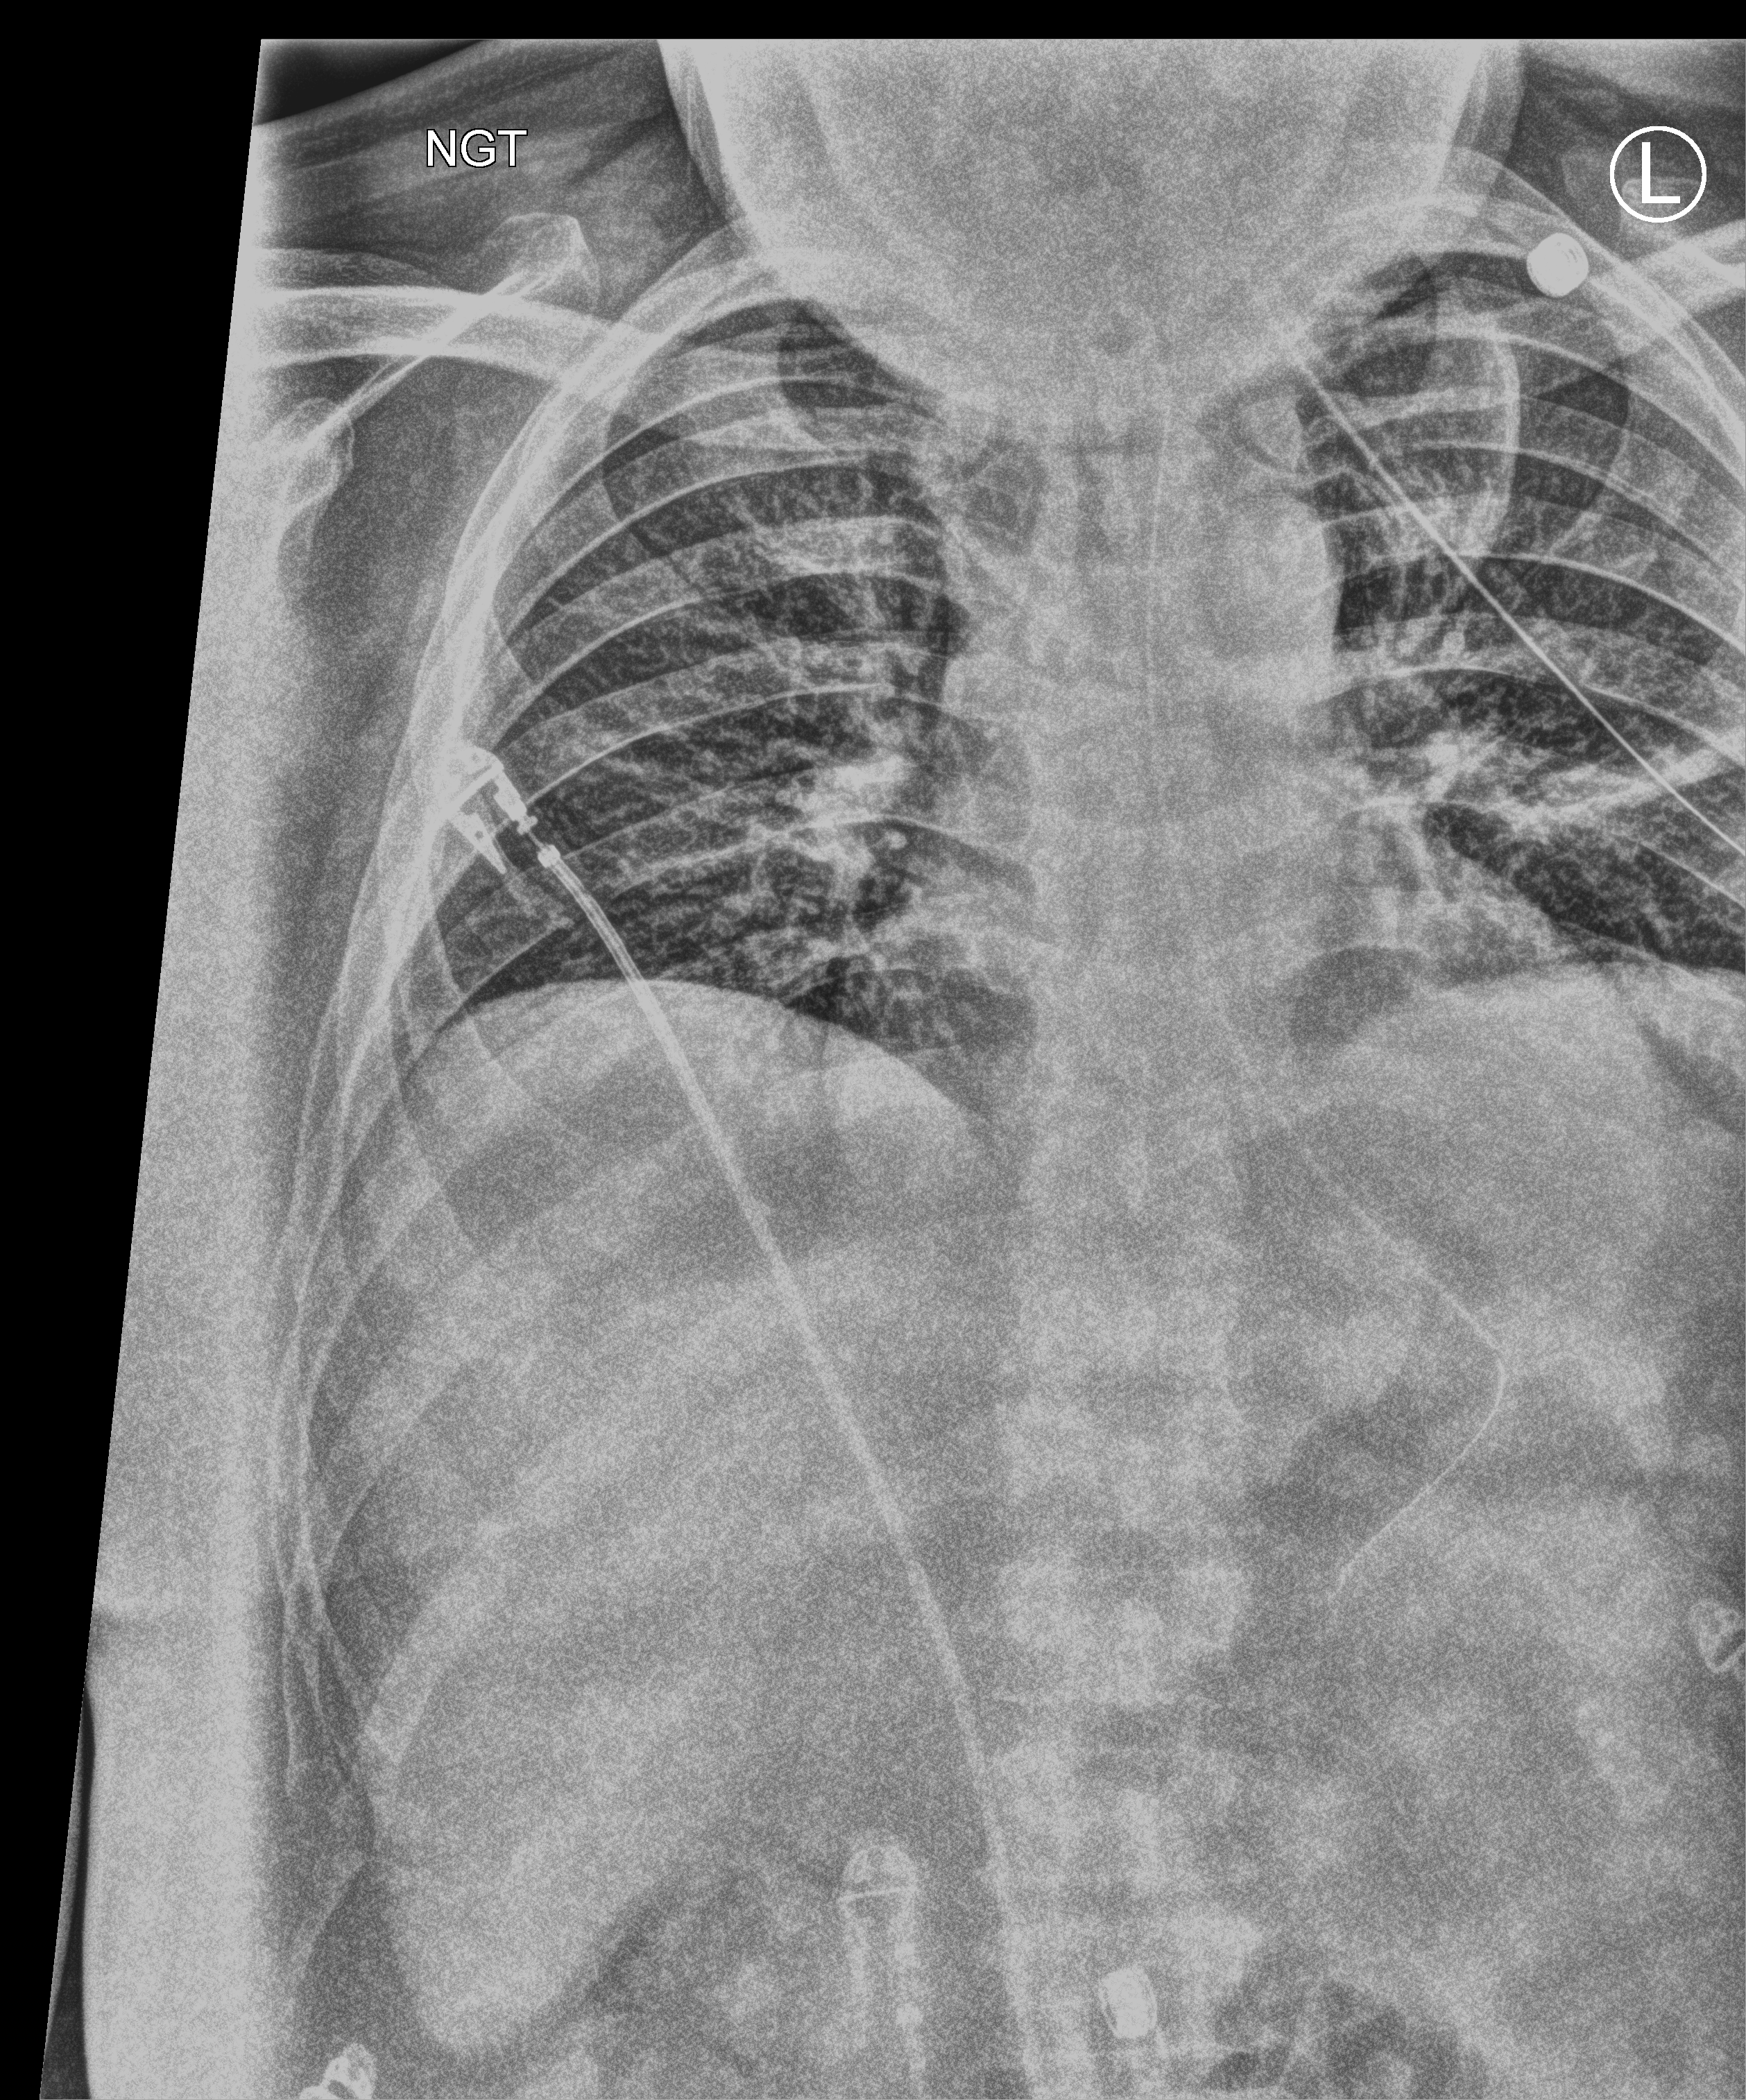
Bedside chest radiograph (computed radiography), anteroposterior (AP) projection. Male patient hospitalised with COVID-19, age 18–59 years.
Admission-level facts for this patient (not findings on this image; timing relative to this image not recorded):
- length of hospital stay: 65 days